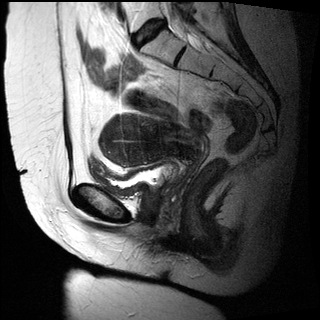
Pelvic MRI for cervical cancer, one sagittal slice. Position 15 of 27 along the scan axis. T2-weighted. 1.5 T. TE 89 ms, TR 2740 ms. 4 mm slice thickness. 320 × 320 image matrix, field of view 260 × 260 mm. Female patient, age 47 years.
Annotated regions visible in this slice (expert manual segmentation):
- uterus and cervix: bounding box <98,114,205,167> (left, top, right, bottom; pixels)